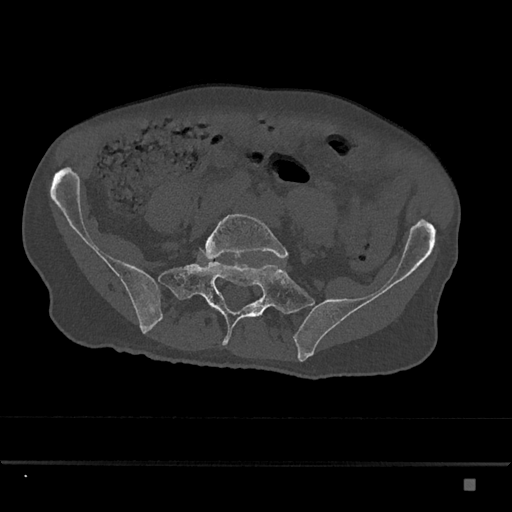
CT including the spine, one axial slice. Position 241 of 797 along the scan axis. Bone window (W 1800 / L 400 HU). 0.5 mm slice thickness. 512 × 512 image matrix, field of view 390 × 390 mm. Patient: male, 72 years. From the clinical record (not read from this slice): primary cancer: prostate.
Structures marked on this image (semi-automatic segmentation, software-assisted and operator-edited):
- L5 vertebra: bounding box [x1, y1, x2, y2] px = [204, 214, 288, 260]